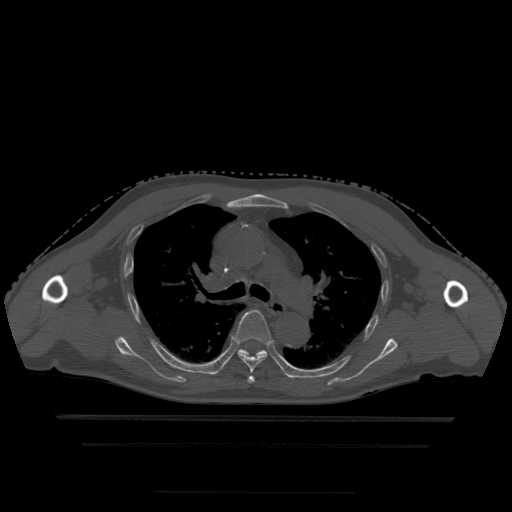
CT including the spine, one axial slice; position 332 of 522 along the scan axis; bone window (W 1800 / L 400 HU); 1.25 mm slice thickness; 512 × 512 image matrix. Patient age 68 years. From the clinical record (not read from this slice): primary cancer: urothelial.
Outlined on this slice (semi-automatically segmented with operator editing):
- T4 vertebra: bounding box (x1, y1, x2, y2) in pixels: (248, 376, 255, 384)
- T5 vertebra: (235, 310, 273, 374)
- T6 vertebra: (239, 349, 267, 357)